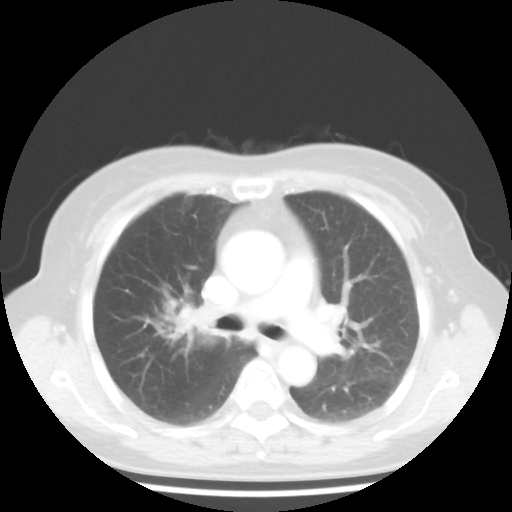
Chest CT, one axial slice. Position 27 of 44 along the scan axis. Reconstruction kernel STANDARD. 100 kVp. Lung window (W 1500 / L -600 HU). 5 mm slice thickness. 512 × 512 image matrix, field of view 316 × 316 mm. Female patient, age 62 years. From the clinical record (not read from this slice): clinical TNM (as recorded): T3 N0 M0; histopathological grade: G3.
Structures marked on this image (bounding box drawn by a radiologist):
- lung tumour (recorded histology: small cell carcinoma): bounding box (x1, y1, x2, y2) in pixels: (171, 300, 211, 347)